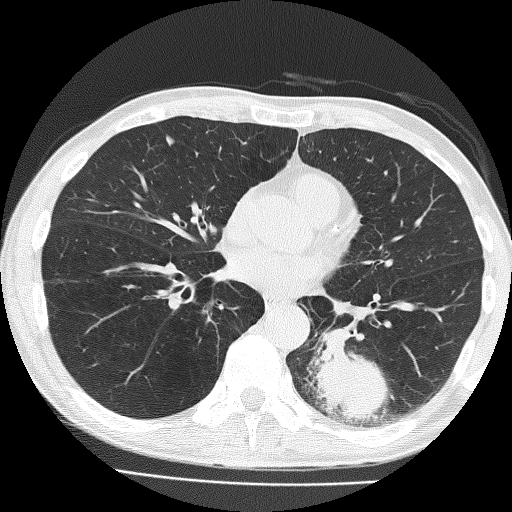
Low-dose screening chest CT, one axial slice. Slice 75 of 160 in the series (ordered by position). Reconstruction kernel FC51. Lung window (W 1500 / L -600 HU). 2 mm slice thickness. 512 × 512 image matrix, field of view 324 × 324 mm.
Structures marked on this image (outlined manually by an expert reader):
- lesion 1 (tumor, lower lobe of left lung): bounding box <310,329,391,424> (left, top, right, bottom; pixels)